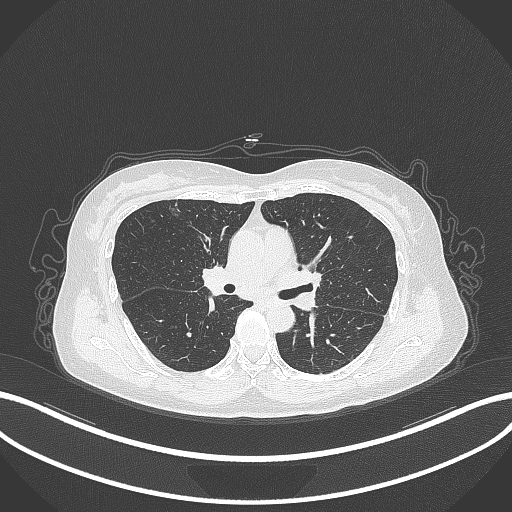
Chest CT, one axial slice. Position 192 of 315 along the scan axis. Reconstruction kernel B70f. Lung window (W 1500 / L -600 HU). 512 × 512 image matrix, field of view 400 × 400 mm. Patient: female, 61 years. Case-level facts recorded for this patient, not image findings: clinical TNM (as recorded): T1b N0 M0.
Structures marked on this image (rectangle marked by the reading radiologist):
- lung tumour (recorded histology: adenocarcinoma): bounding box (x1, y1, x2, y2) in pixels: (163, 199, 183, 222)